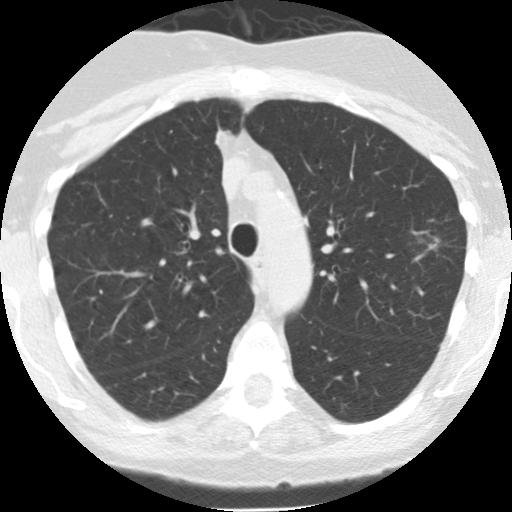
Low-dose screening chest CT, one axial slice; slice 105 of 145 in the series (ordered by position); reconstruction kernel STANDARD; 120 kVp; lung window (W 1500 / L -600 HU); 2.5 mm slice thickness; 512 × 512 image matrix, field of view 280 × 280 mm.
Structures marked on this image (outlined manually by an expert reader):
- lesion 1 (tumor, upper lobe of left lung): bounding box [x1, y1, x2, y2] px = [429, 238, 439, 250]